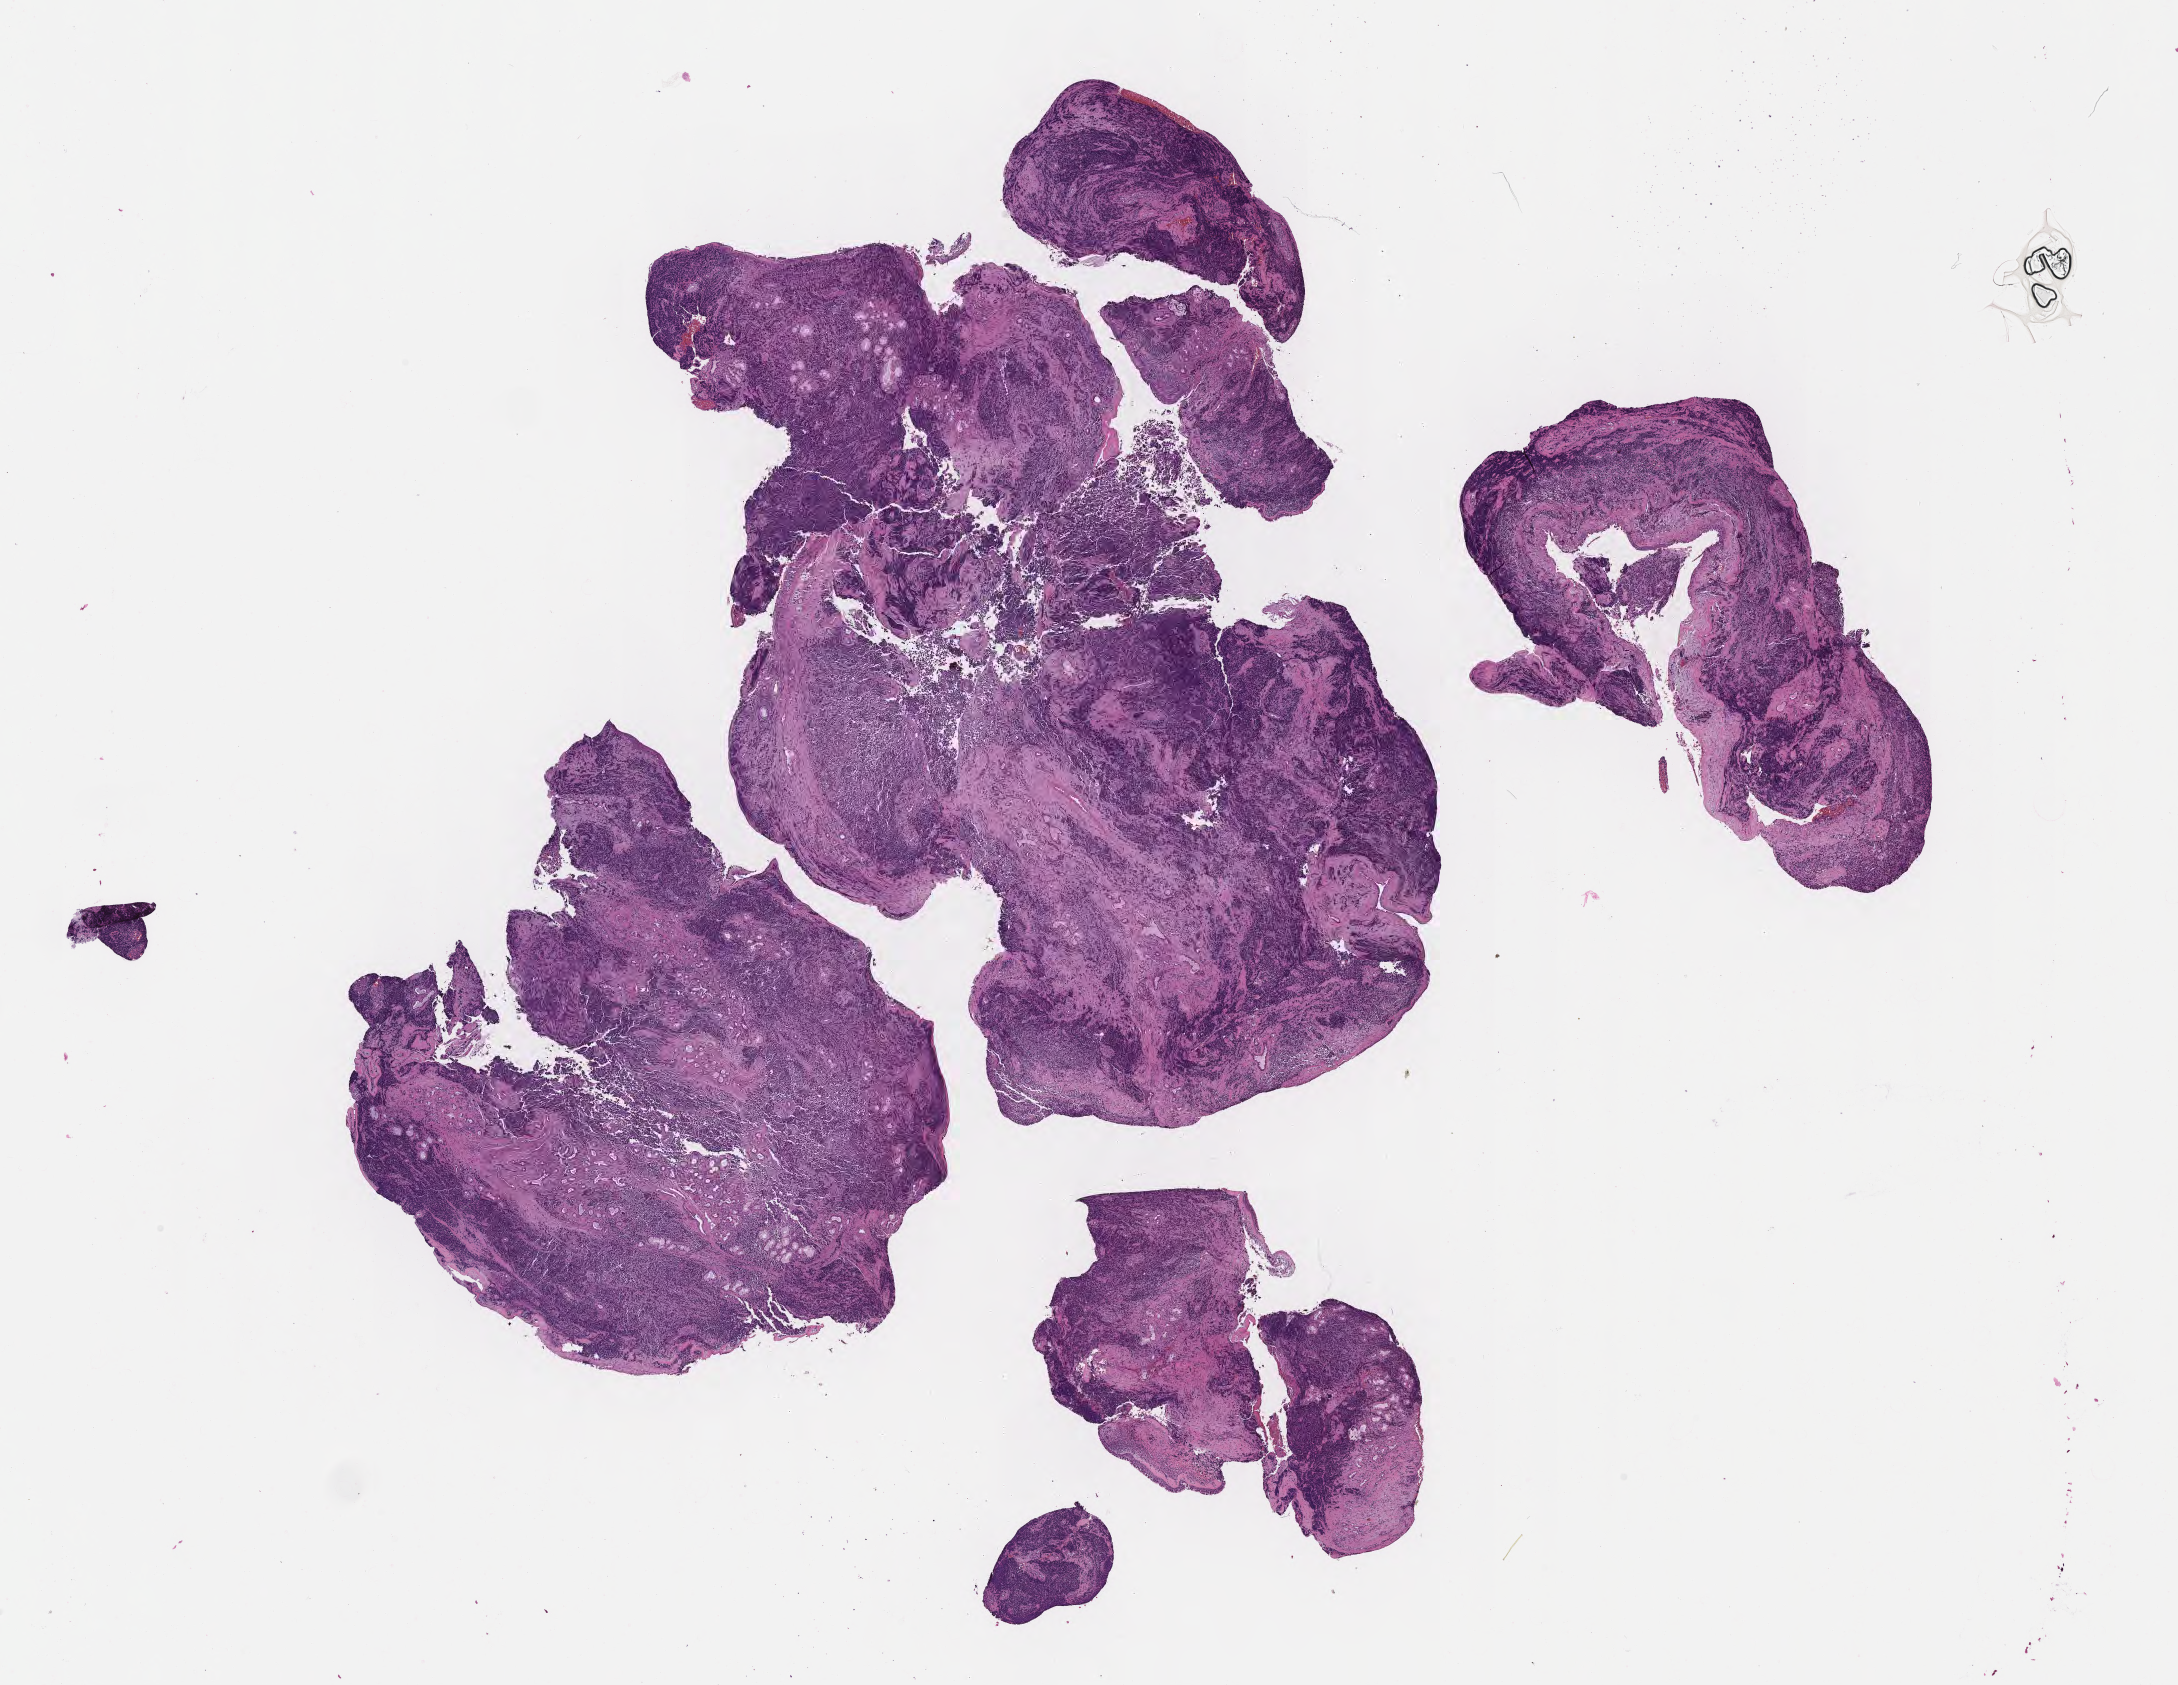
Digitized H&E-stained section of tumor tissue from the nasal sinus — a low-resolution overview of the entire scanned area, about 17.6 x 13.6 mm, formalin-fixed, paraffin-embedded (FFPE) tissue. Female patient, age 249 months.
Diagnosis: Rhabdomyosarcoma, NOS.